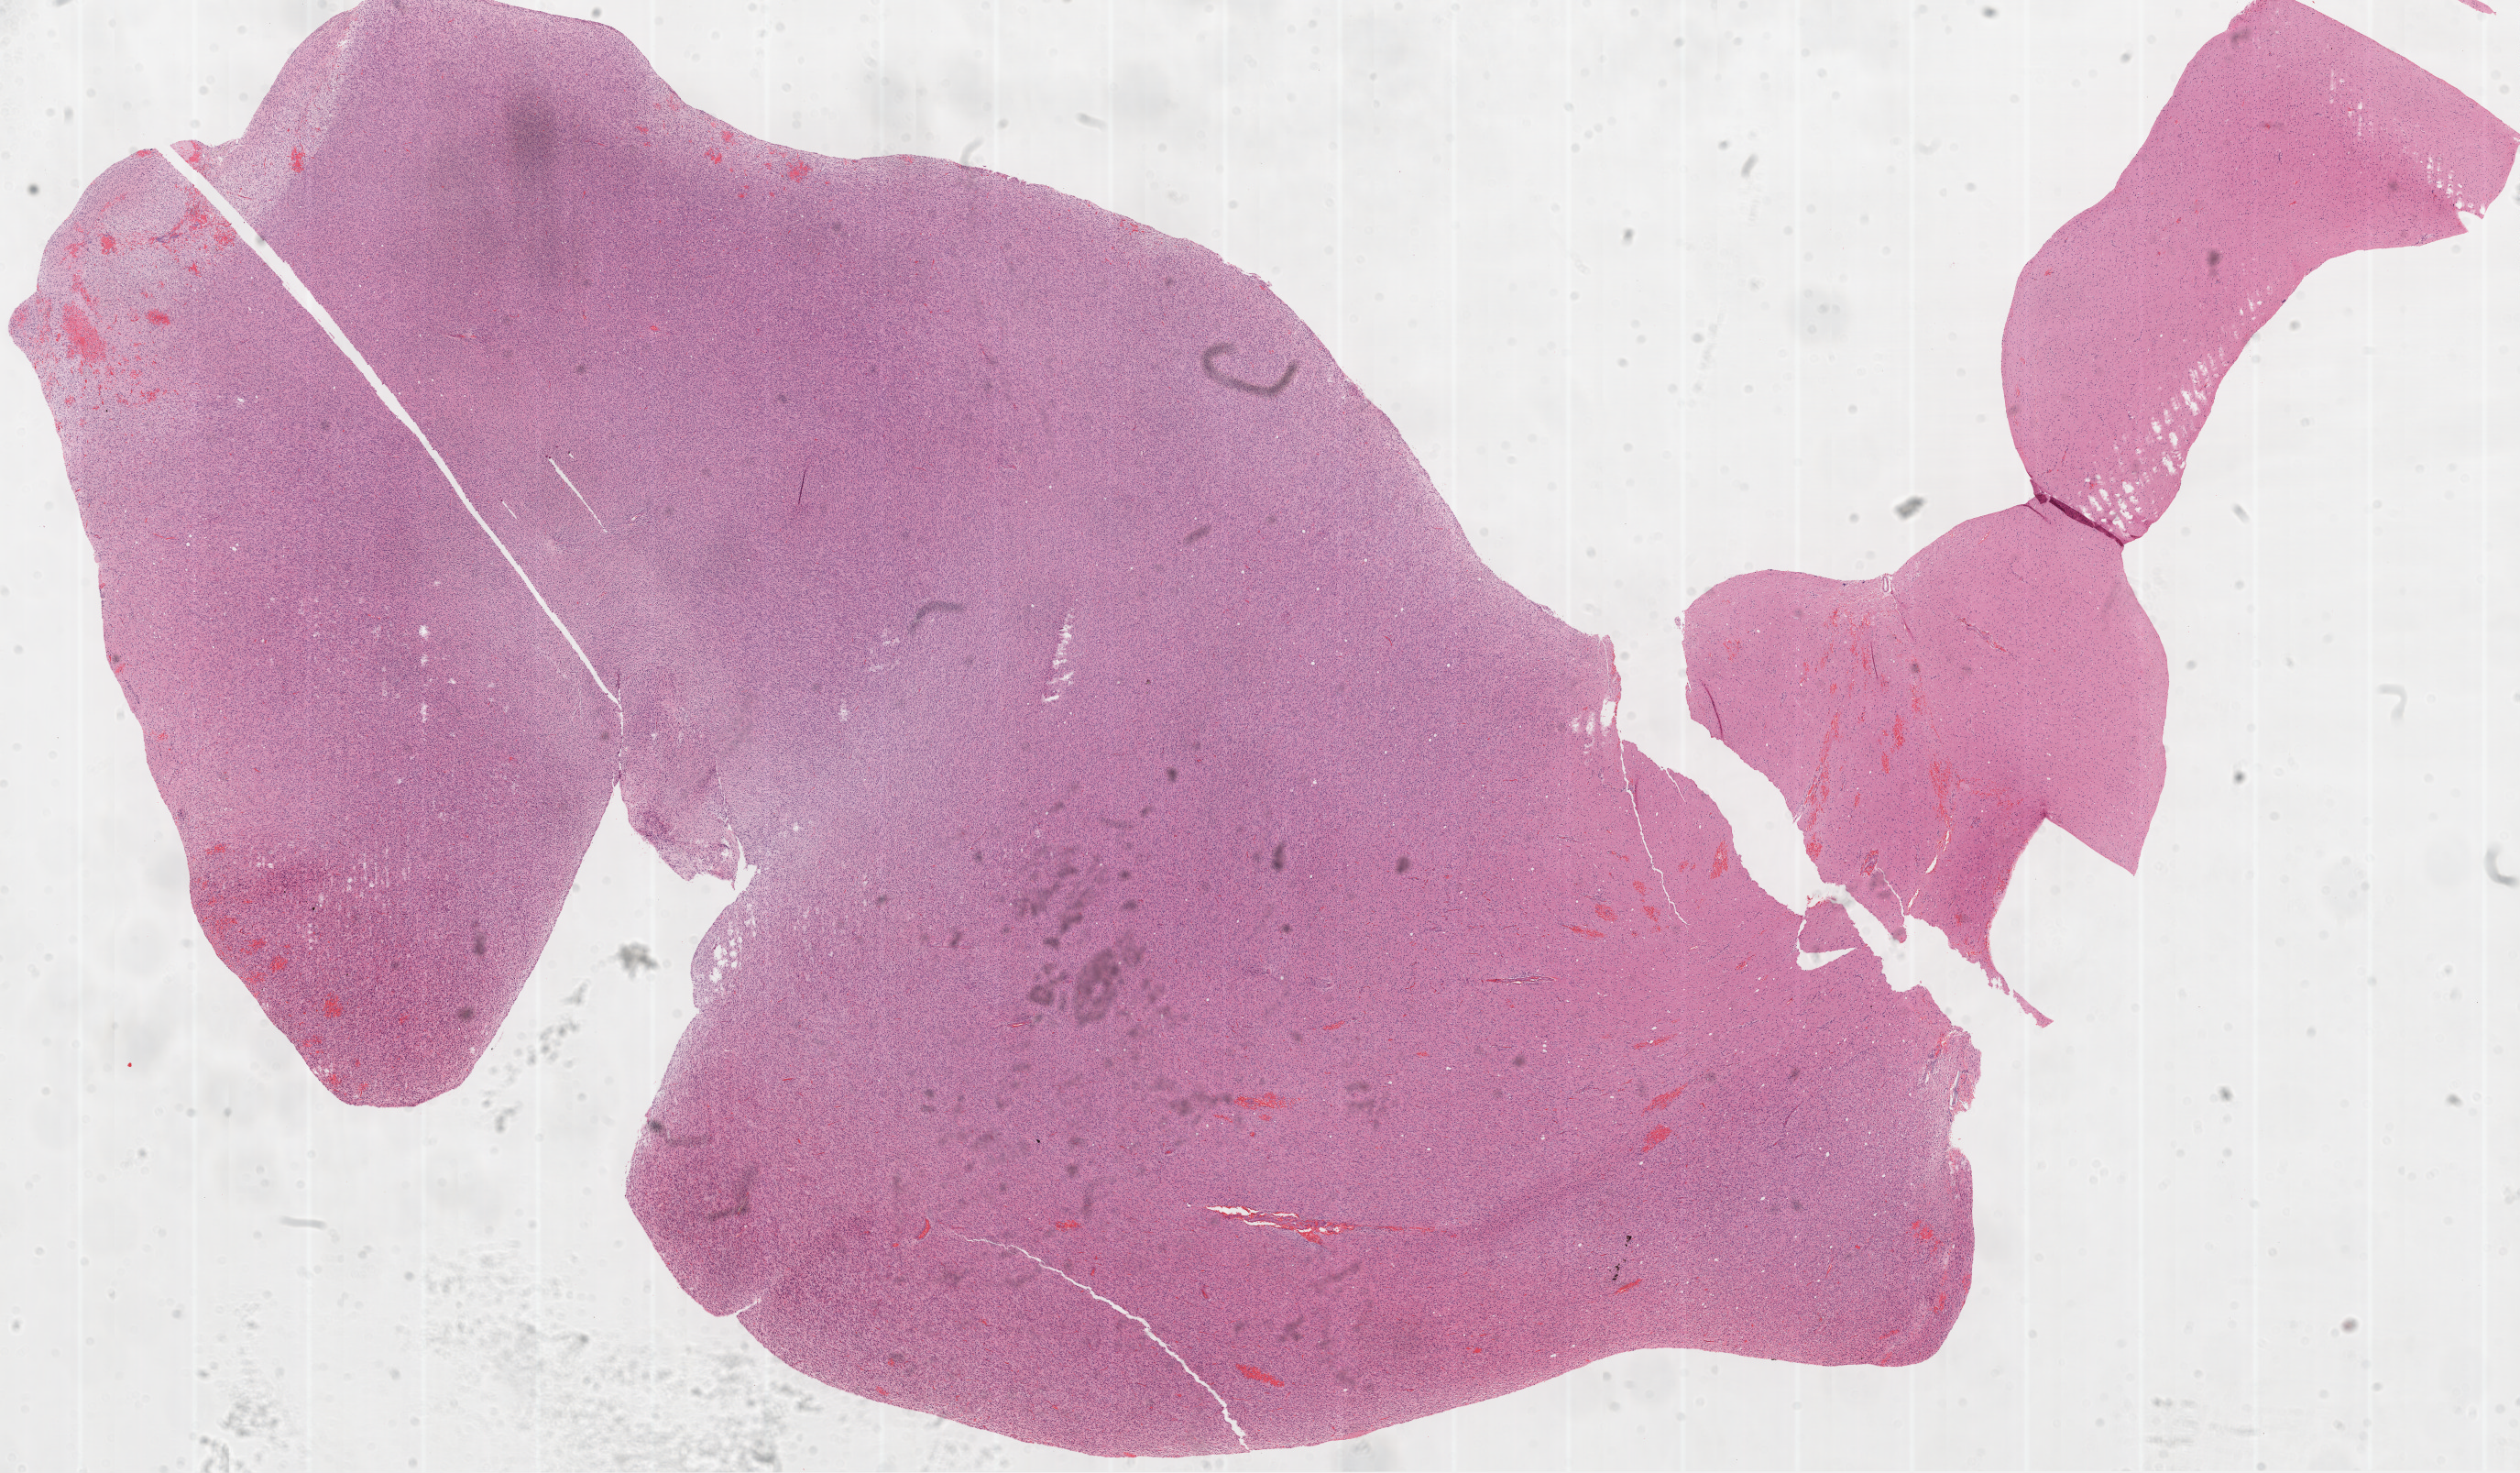
H&E-stained whole-slide image, whole scanned area (about 22.1 x 12.9 mm, from a 20x scan) shown as a low-resolution overview. FFPE section. Brain, primary tumour sample. Female patient; age at initial diagnosis 61 years.
Pathologic diagnosis: Glioblastoma.